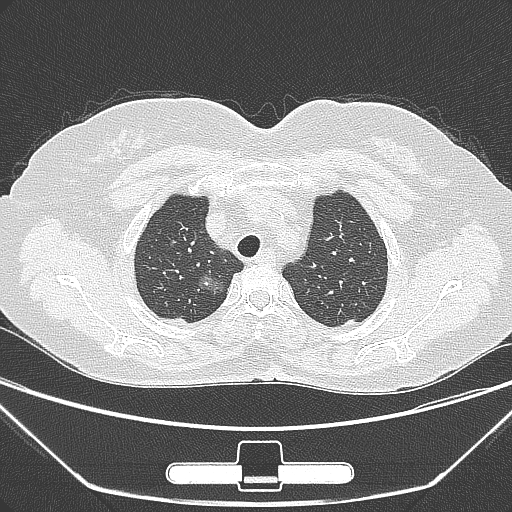
Chest CT, one axial slice. Position 231 of 275 along the scan axis. 120 kVp. Lung window (W 1500 / L -600 HU). 512 × 512 image matrix, field of view 356 × 356 mm. Female patient, age 63 years. From the clinical record (not read from this slice): clinical TNM (as recorded): T1a N0 M0; histopathological grade: G1.
Structures marked on this image (rectangle marked by the reading radiologist):
- lung tumour (recorded histology: adenocarcinoma): bounding box [x1, y1, x2, y2] px = [195, 265, 238, 313]